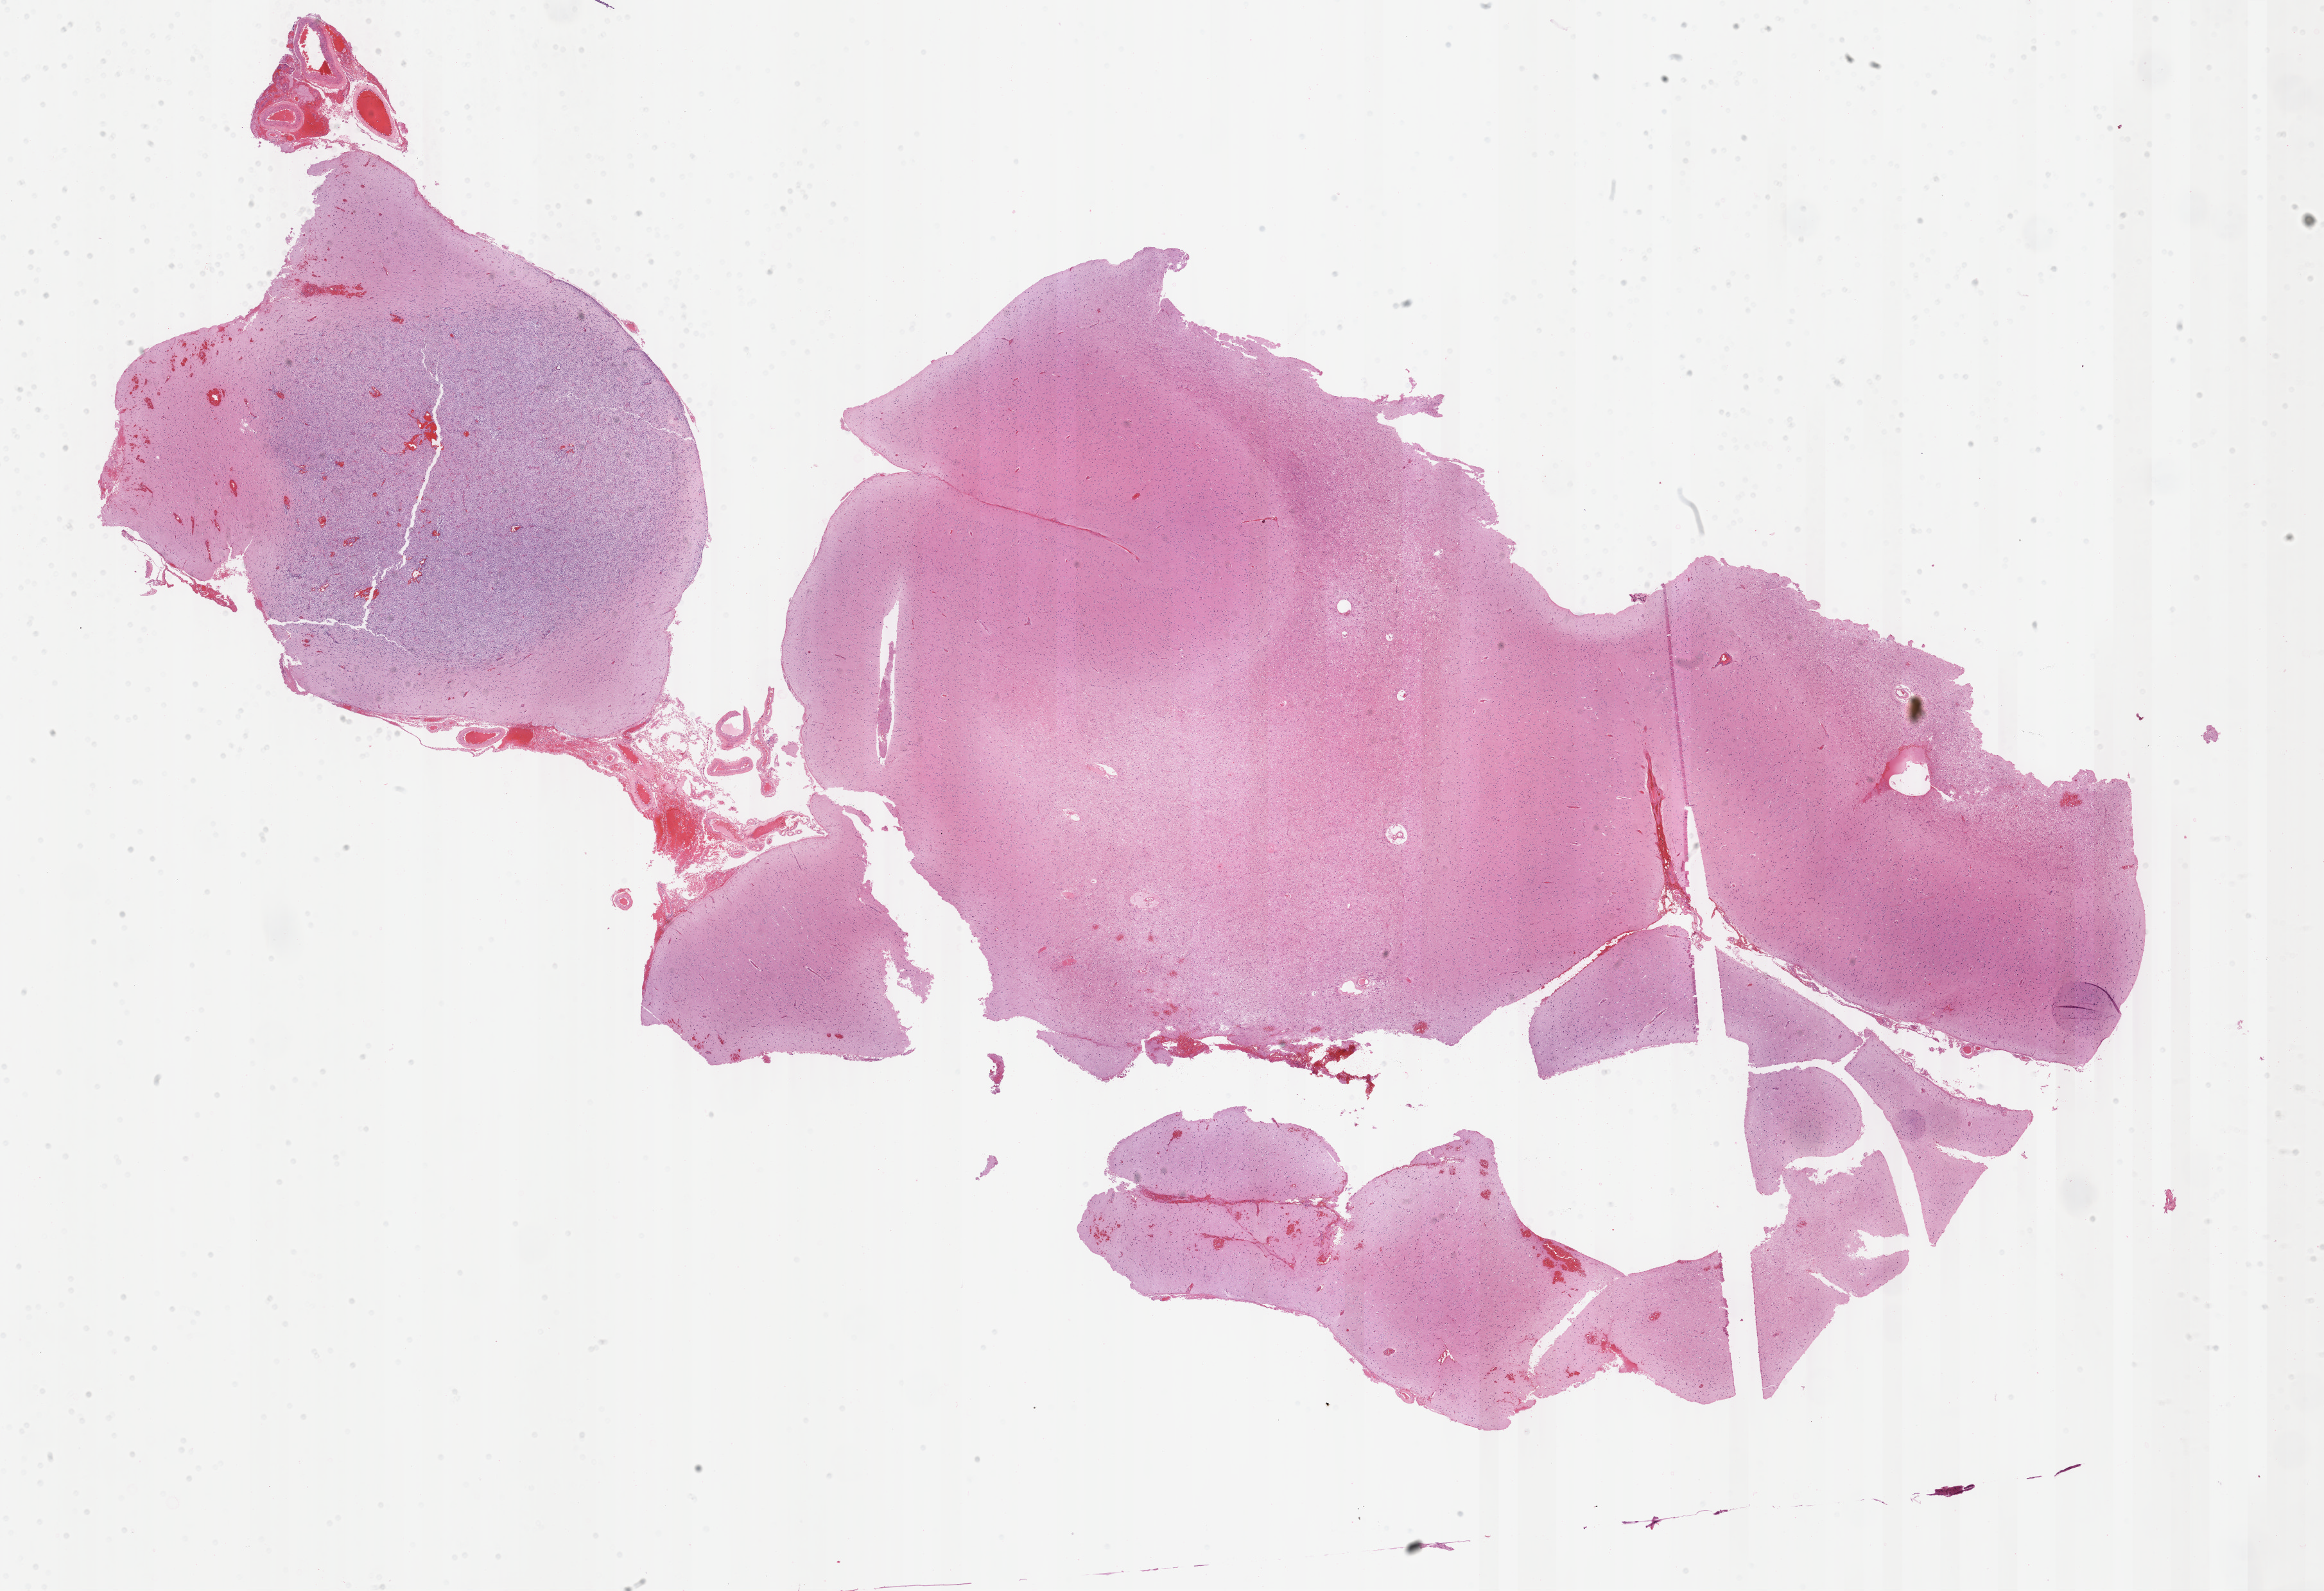
Whole-slide histology image, H&E-stained — a low-resolution overview of the entire scanned area, about 28.8 x 19.7 mm (from a 40x scan); FFPE section; primary tumour sample from the brain. Patient: male, age at initial diagnosis 74 years.
Diagnosis: Glioblastoma.